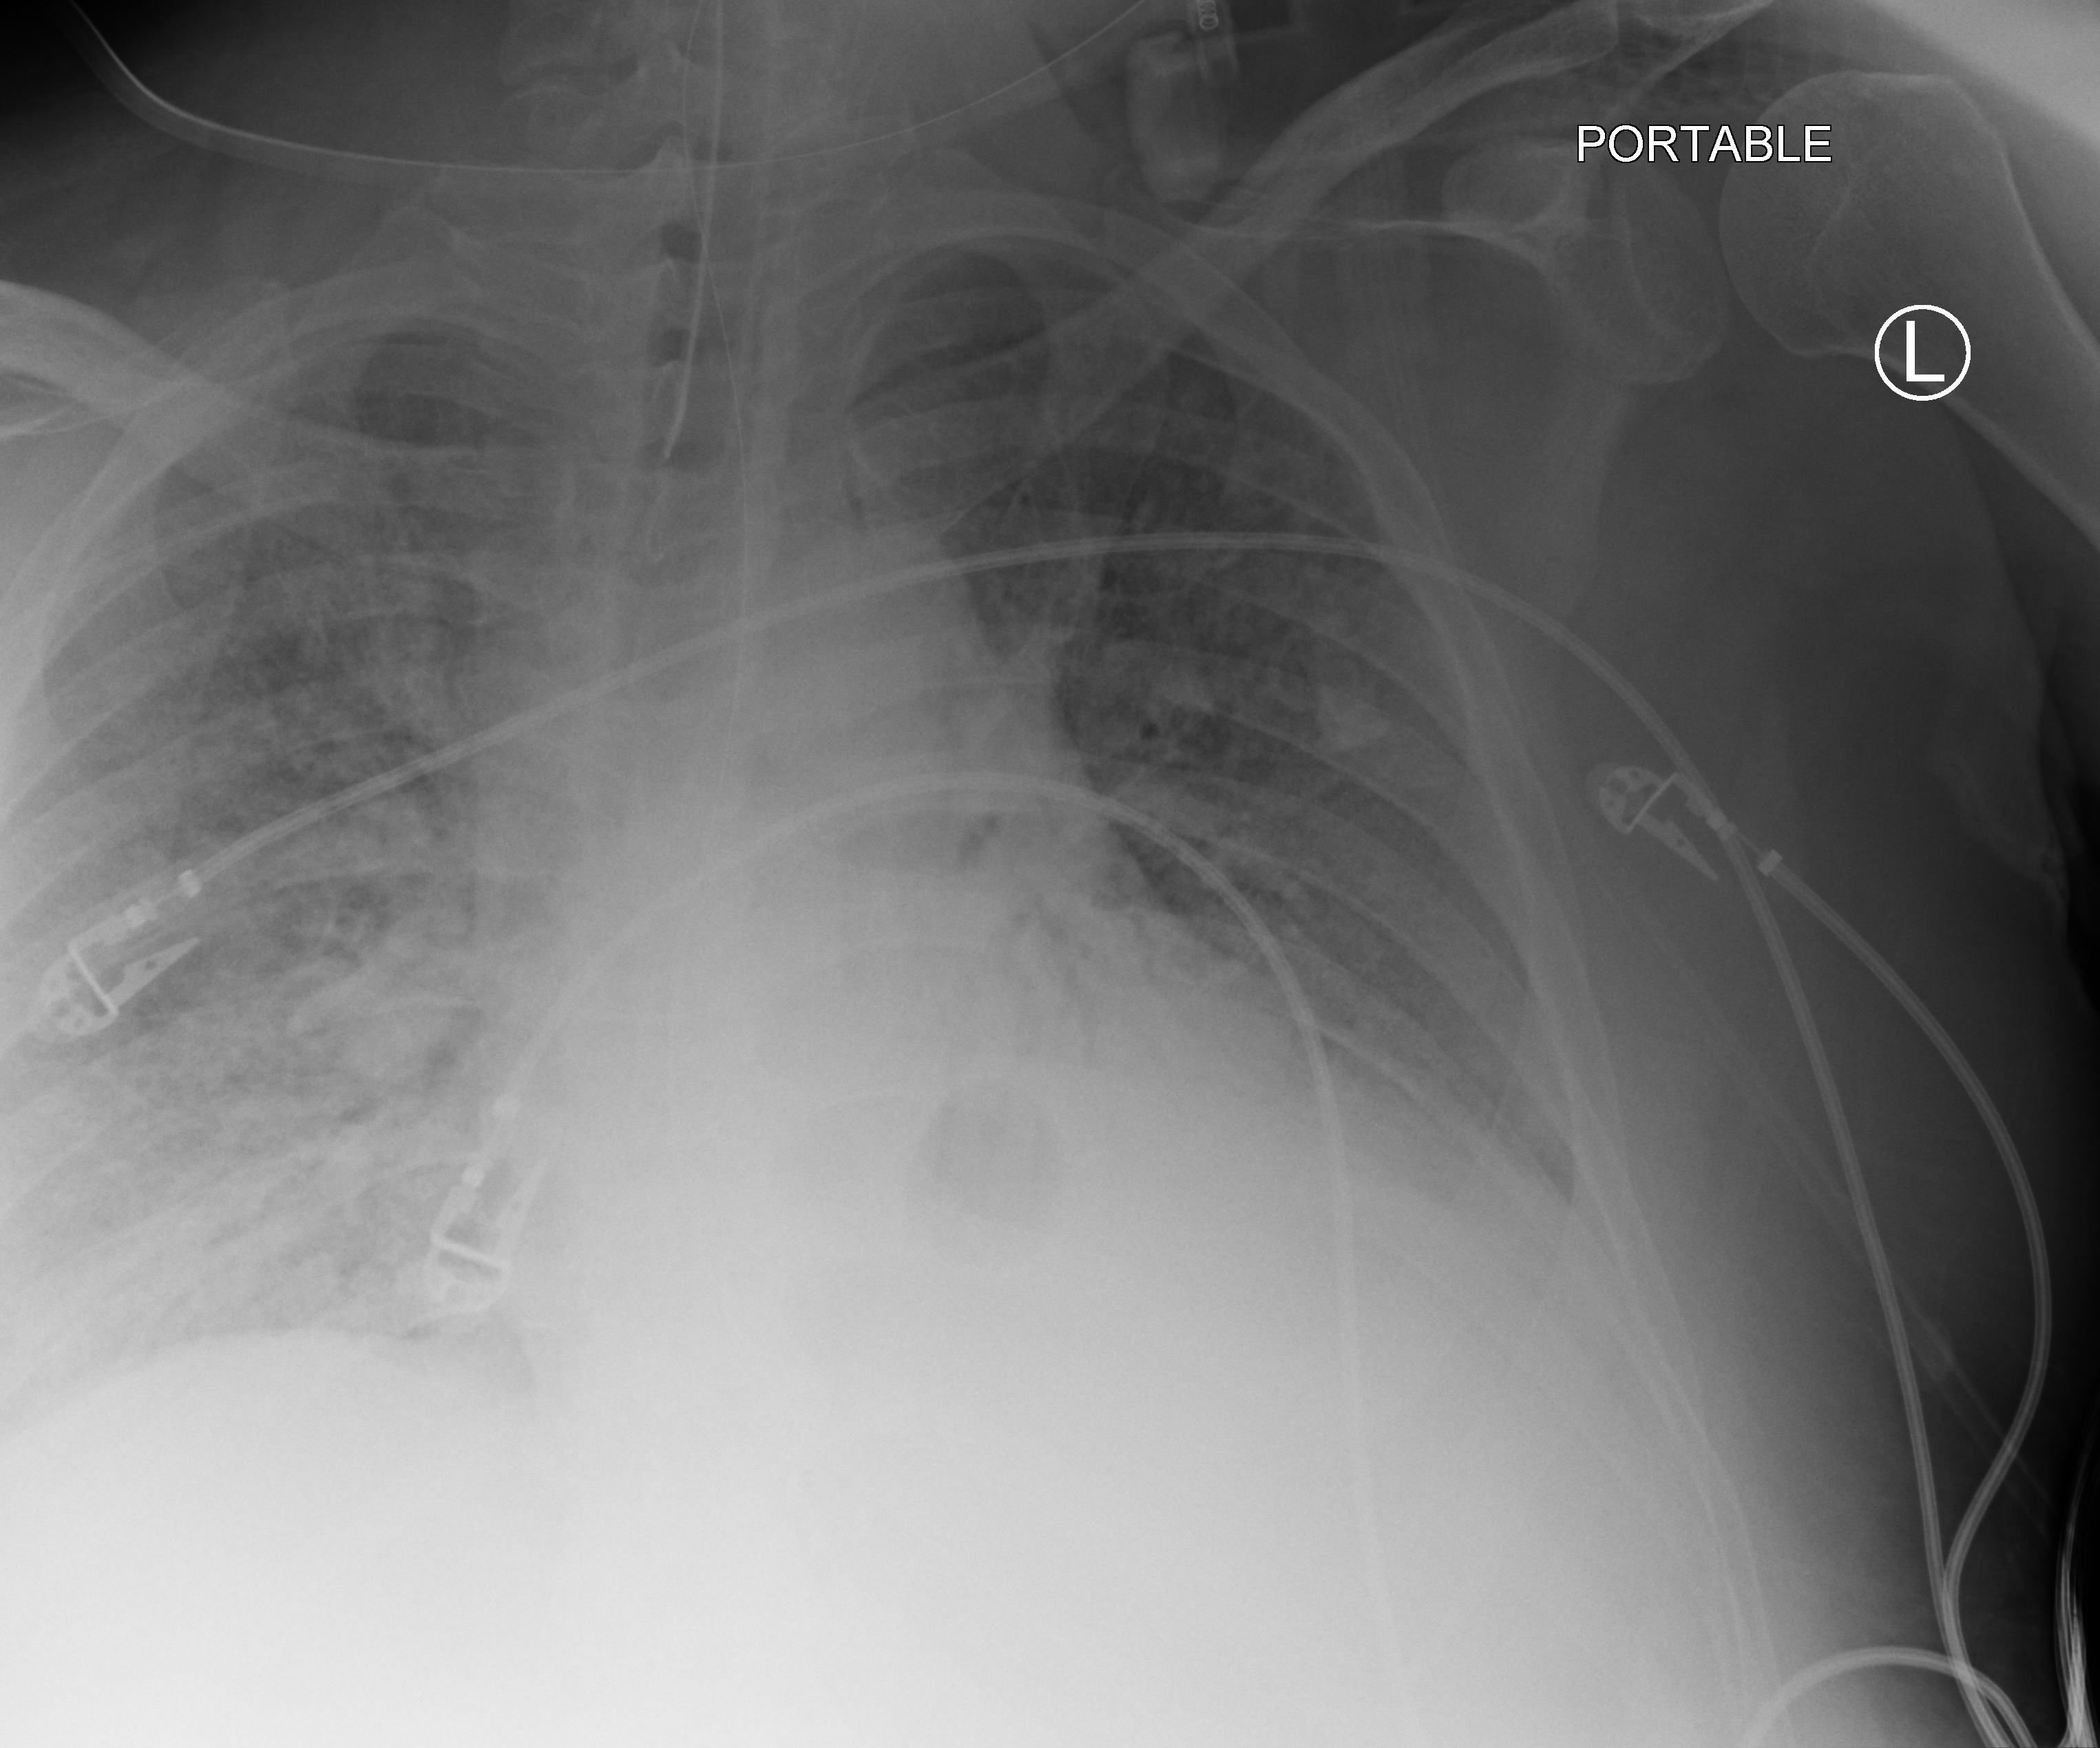
Chest X-ray (portable). Patient hospitalised with COVID-19, aged 18–59 years.
Admission-level facts for this patient (not findings on this image; timing relative to this image not recorded): admitted to intensive care during this hospital stay: yes; mechanically ventilated during this hospital stay: yes.